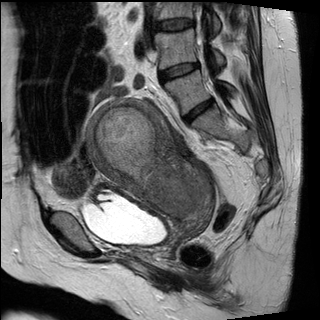
Pelvic MRI for cervical cancer, one sagittal slice; position 17 of 30 along the scan axis; T2-weighted; 1.5 T; TE 89 ms, TR 2930 ms; 320 × 320 image matrix. Female patient, age 62 years.
Annotated regions visible in this slice (manually delineated by an expert):
- uterus and cervix: bounding box <85,97,211,218> (left, top, right, bottom; pixels)